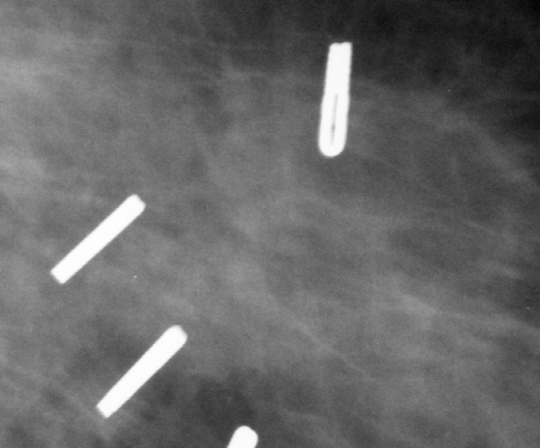
Cropped region of a digitized screen-film mammogram centred on a radiologist-marked abnormality; left breast; MLO view.
Marked abnormality: mass, shape architectural distortion, margins ill defined; BI-RADS assessment category 2; subtlety rating 5 on a 1 (subtle) to 5 (obvious) scale; benign; no additional work-up was recommended (benign without callback).